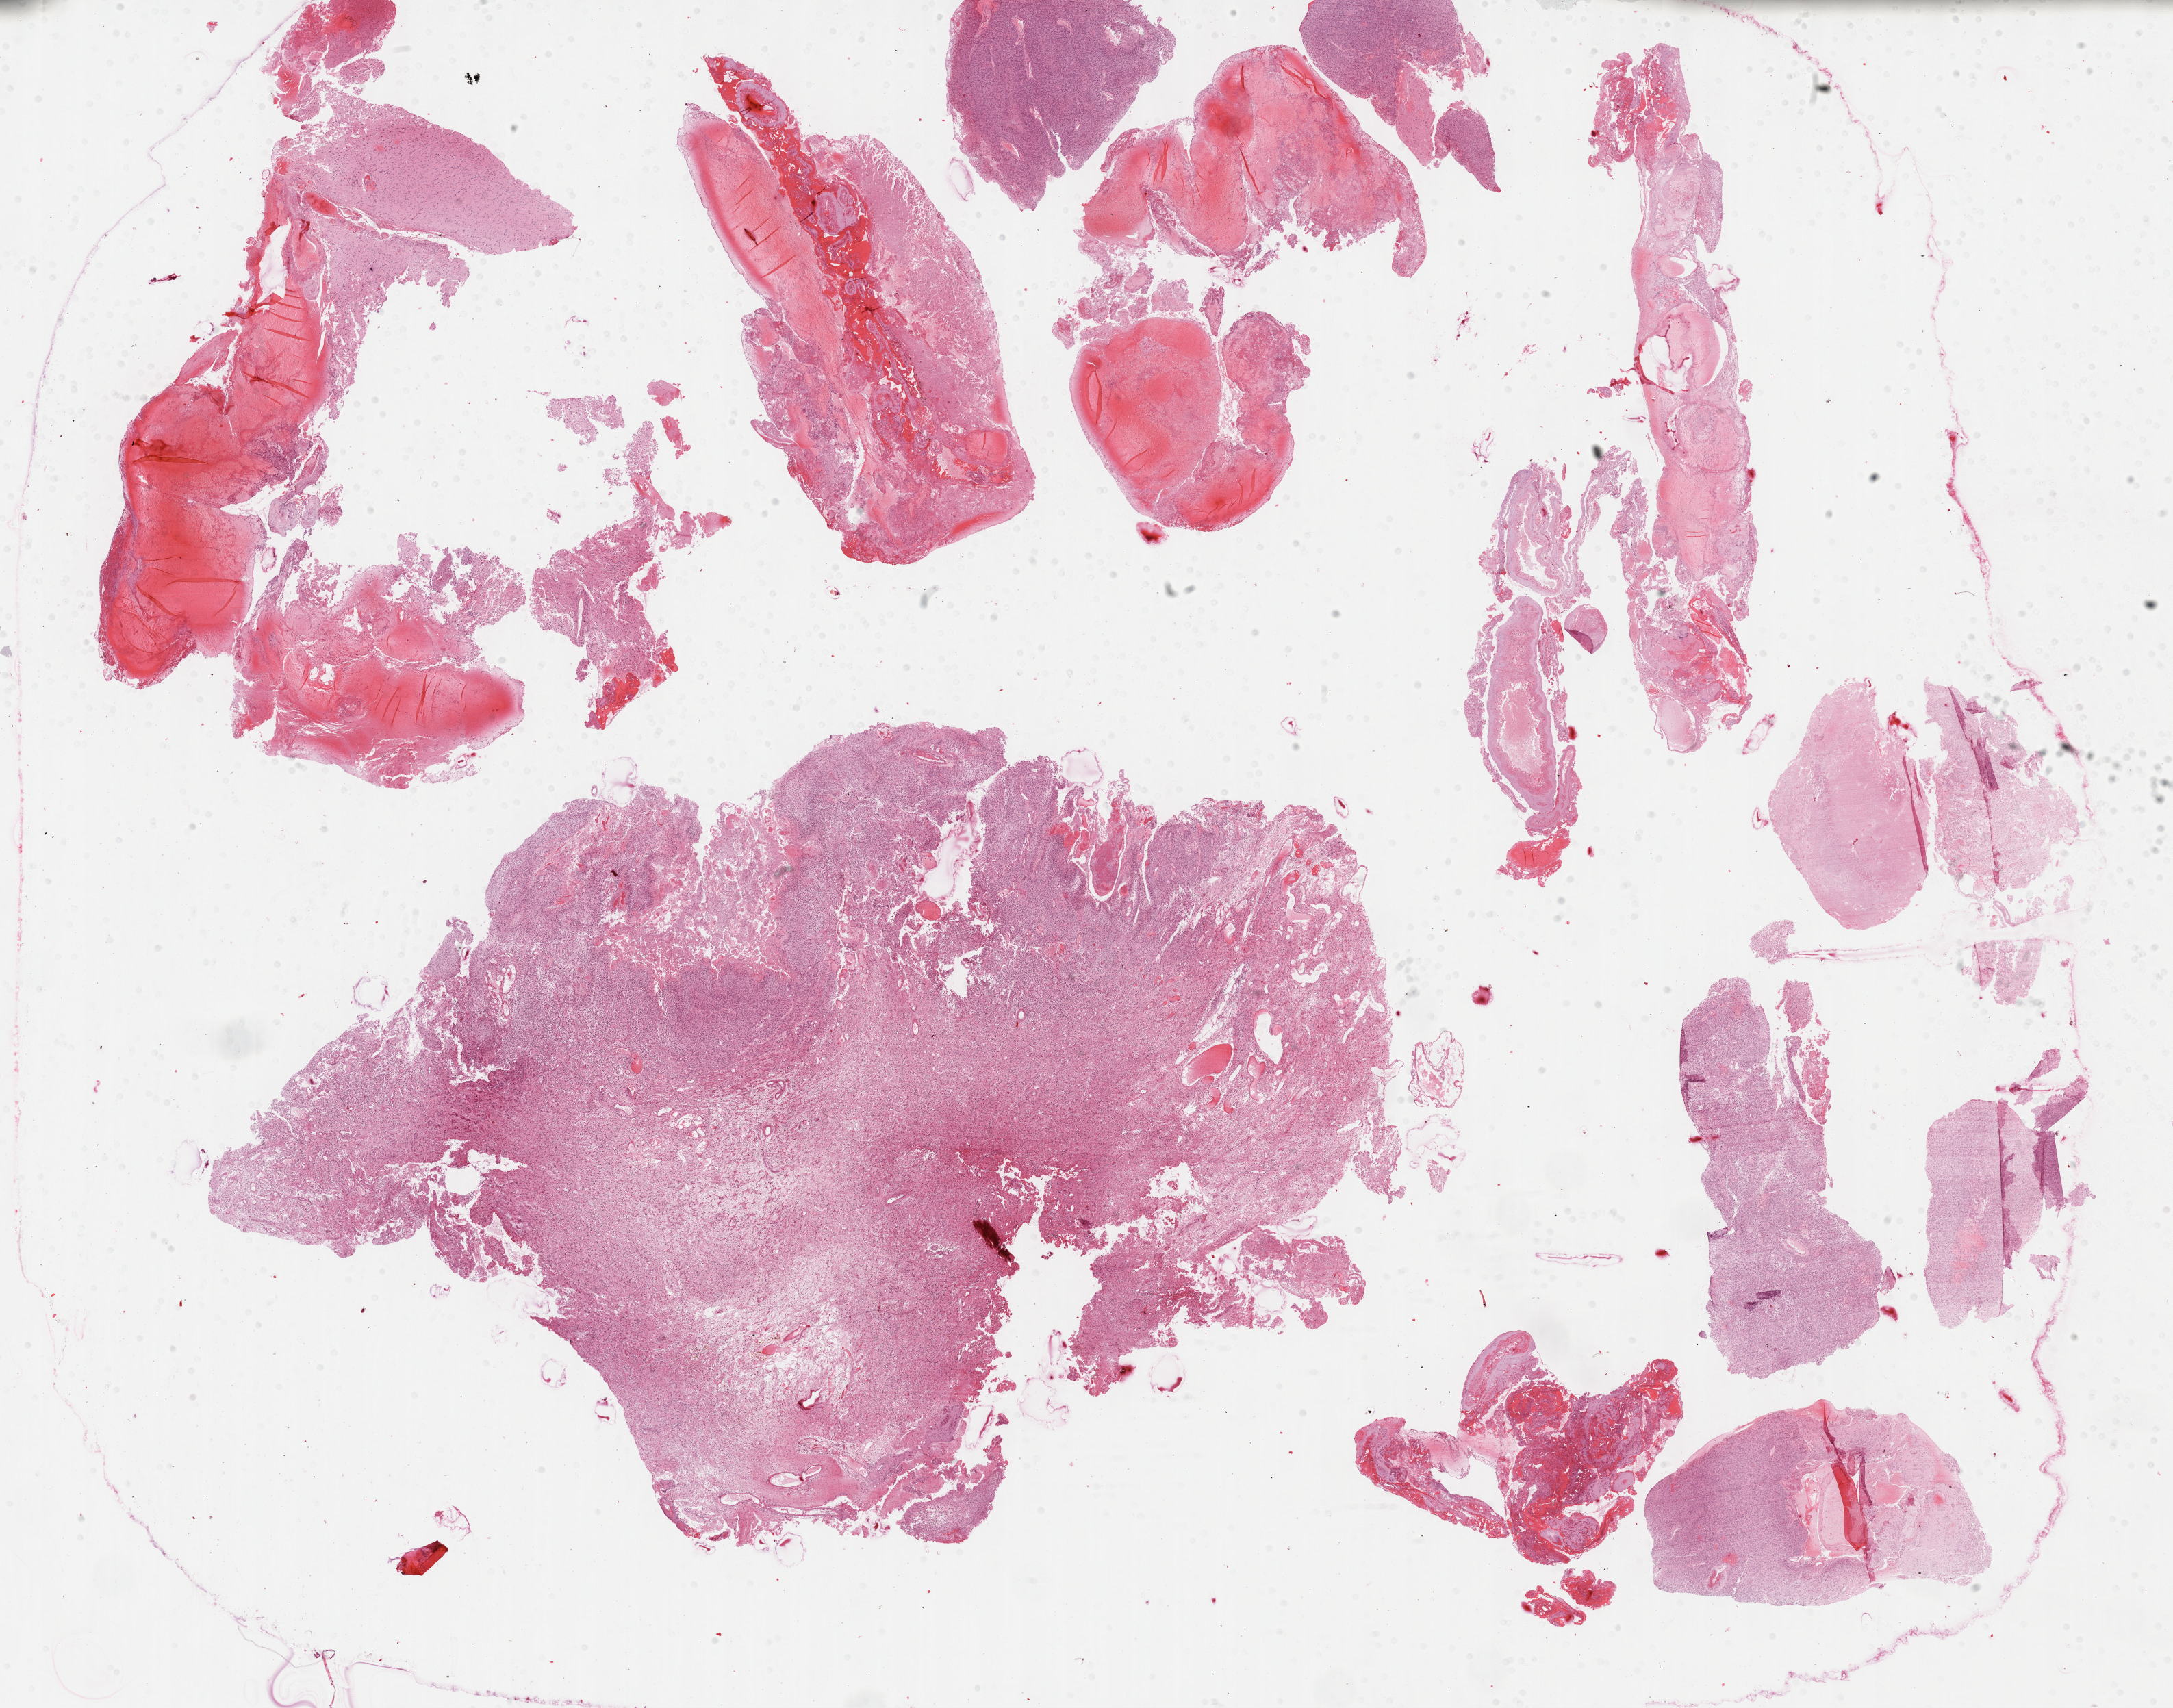
Digitized H&E-stained tissue section (whole slide) — whole scanned area (about 25.7 x 20.2 mm) shown as a low-resolution overview; formalin-fixed paraffin-embedded (FFPE) diagnostic section; primary tumour sample from the brain. Male, age 62 years at initial diagnosis.
Histologic diagnosis: Glioblastoma.